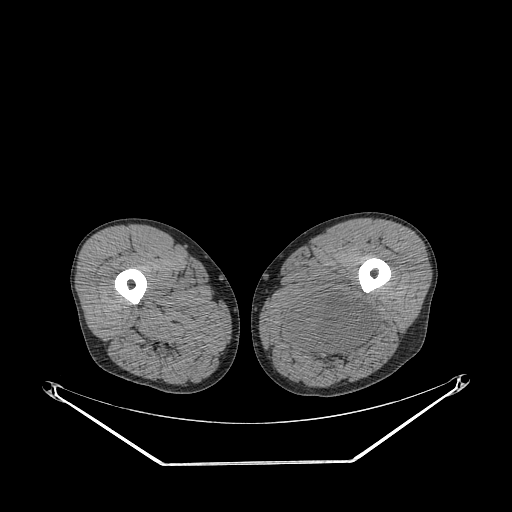
CT of an extremity soft-tissue mass (from a PET/CT study), one axial slice; slice 250 of 267 in the series (ordered by position); reconstruction kernel STANDARD; 140 kVp; soft-tissue window (W 400 / L 40 HU); 3.75 mm slice thickness; 512 × 512 image matrix, field of view 500 × 500 mm. Male patient. From the clinical record (not read from this slice): histological type: undifferentiated pleomorphic liposarcoma; grade: high; site of the primary tumour: left thigh.
Annotated regions visible in this slice (expert contour drawn on MRI and transferred to this co-registered scan by the dataset authors):
- gross tumour volume including surrounding oedema: bounding box [x1, y1, x2, y2] px = [279, 288, 375, 359]
- gross tumour volume (mass): [290, 290, 373, 350]